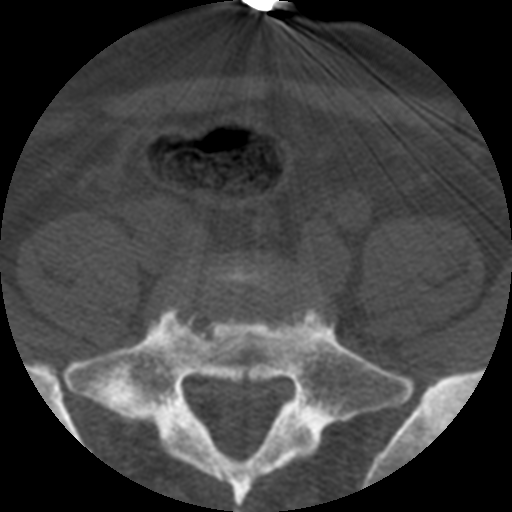
CT including the spine, one axial slice; position 46 of 508 along the scan axis; 120 kVp; bone window (W 1800 / L 400 HU); 1.25 mm slice thickness; 512 × 512 image matrix, field of view 160 × 160 mm. Patient age 57 years. From the clinical record (not read from this slice): primary cancer: prostate.
Structures marked on this image (semi-automatically segmented with operator editing):
- L5 vertebra: bounding box (x1, y1, x2, y2) in pixels: (191, 258, 306, 288)